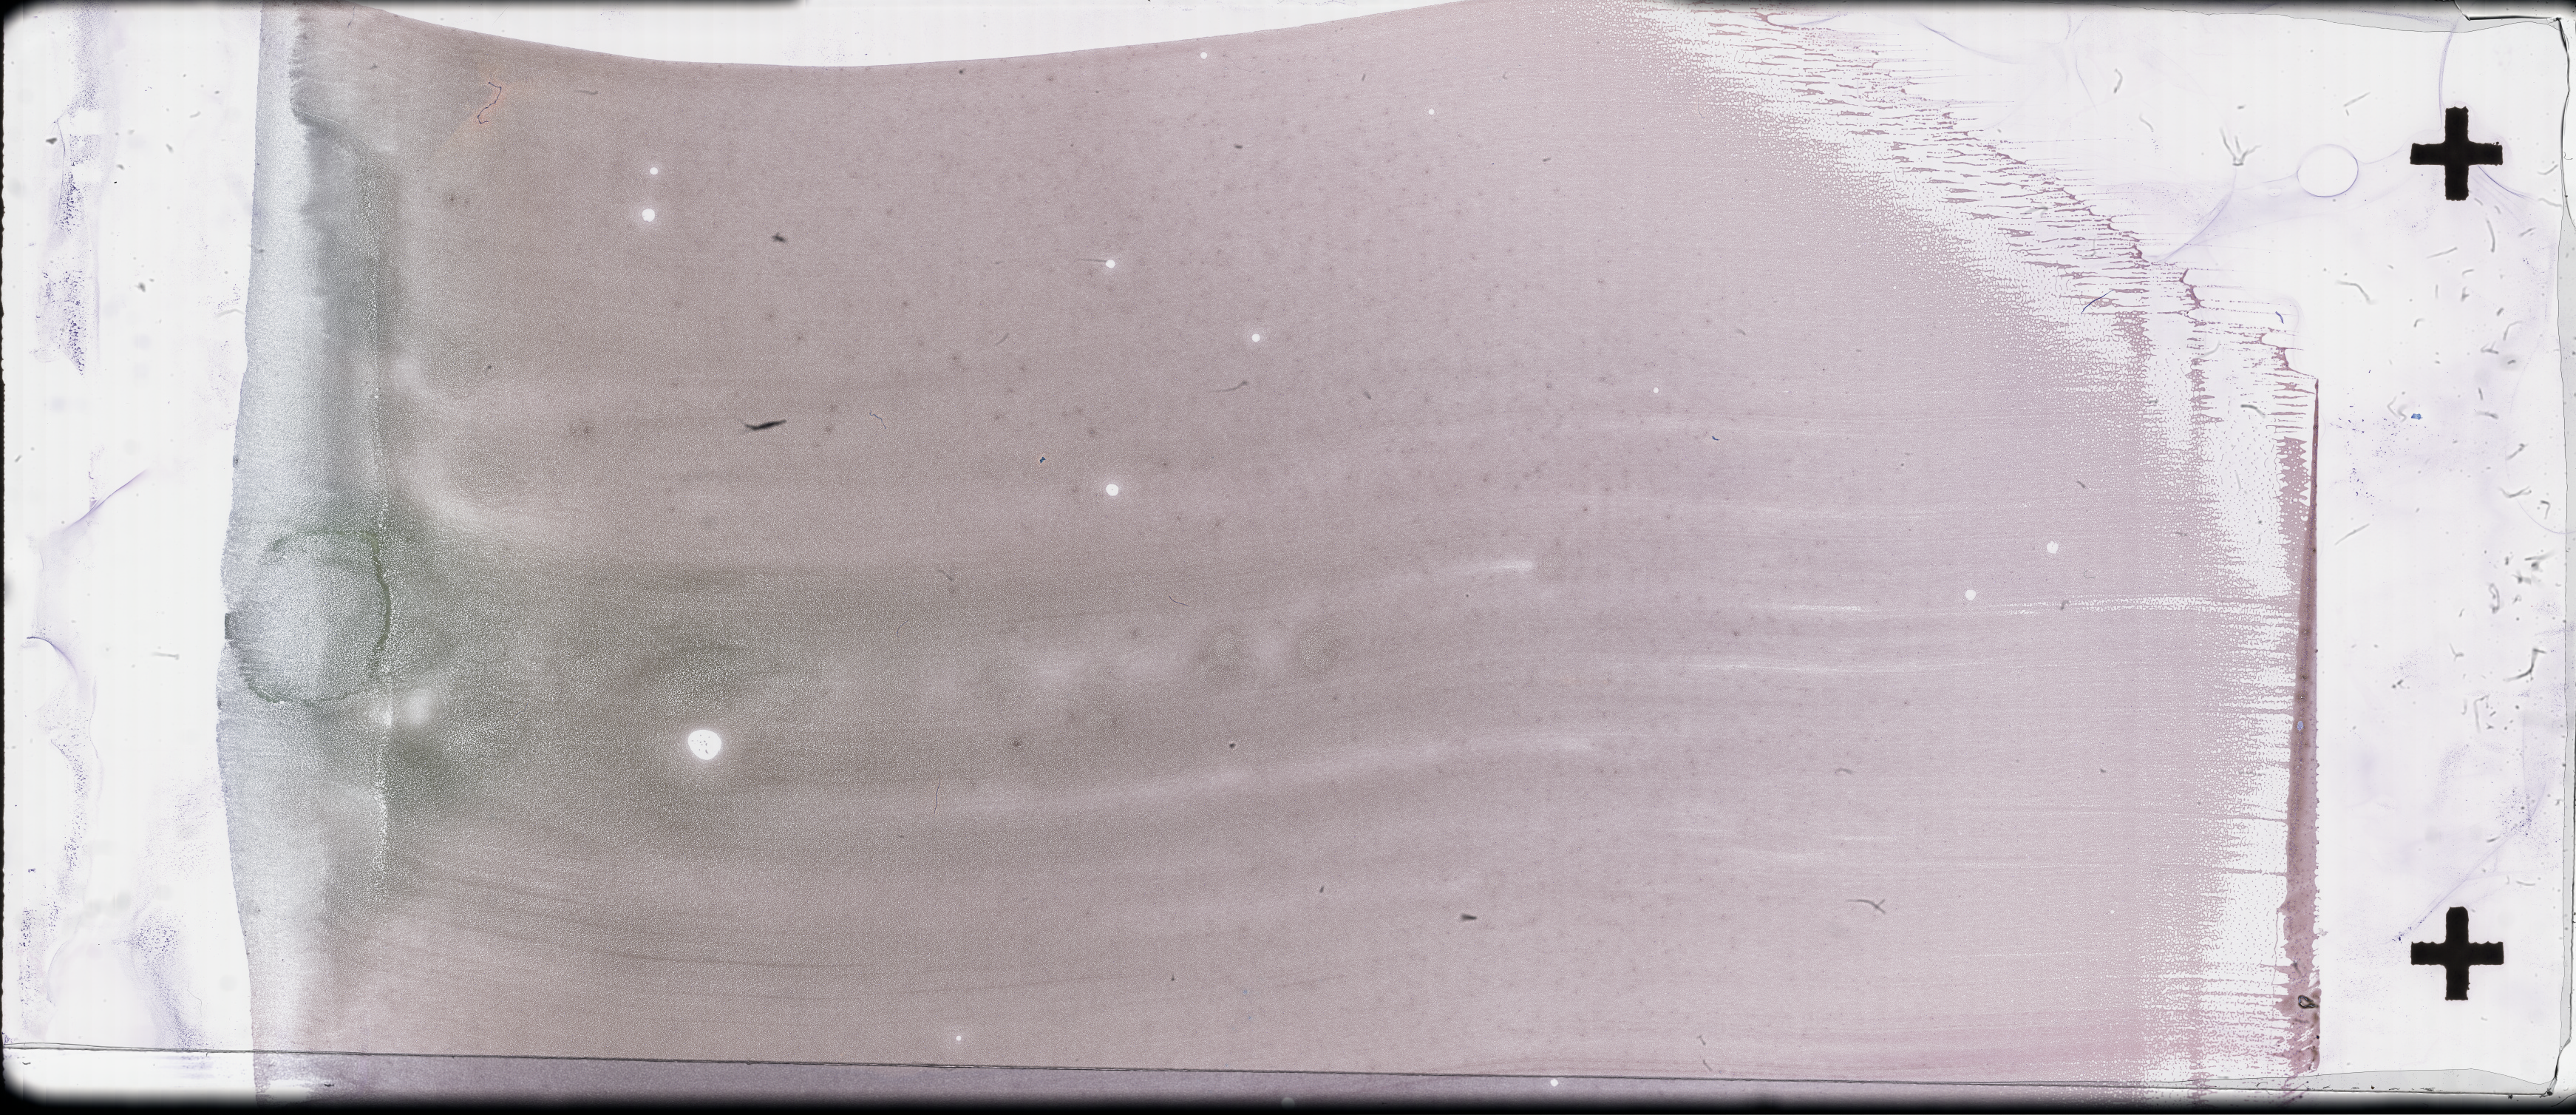
Wright-Giemsa-stained whole blood smear, whole-slide image — low-resolution overview of the scanned area, about 56.3 x 24.4 mm. EDTA-anticoagulated smear. Patient sex: male.
From a patient with: Plasma Cell Myeloma.